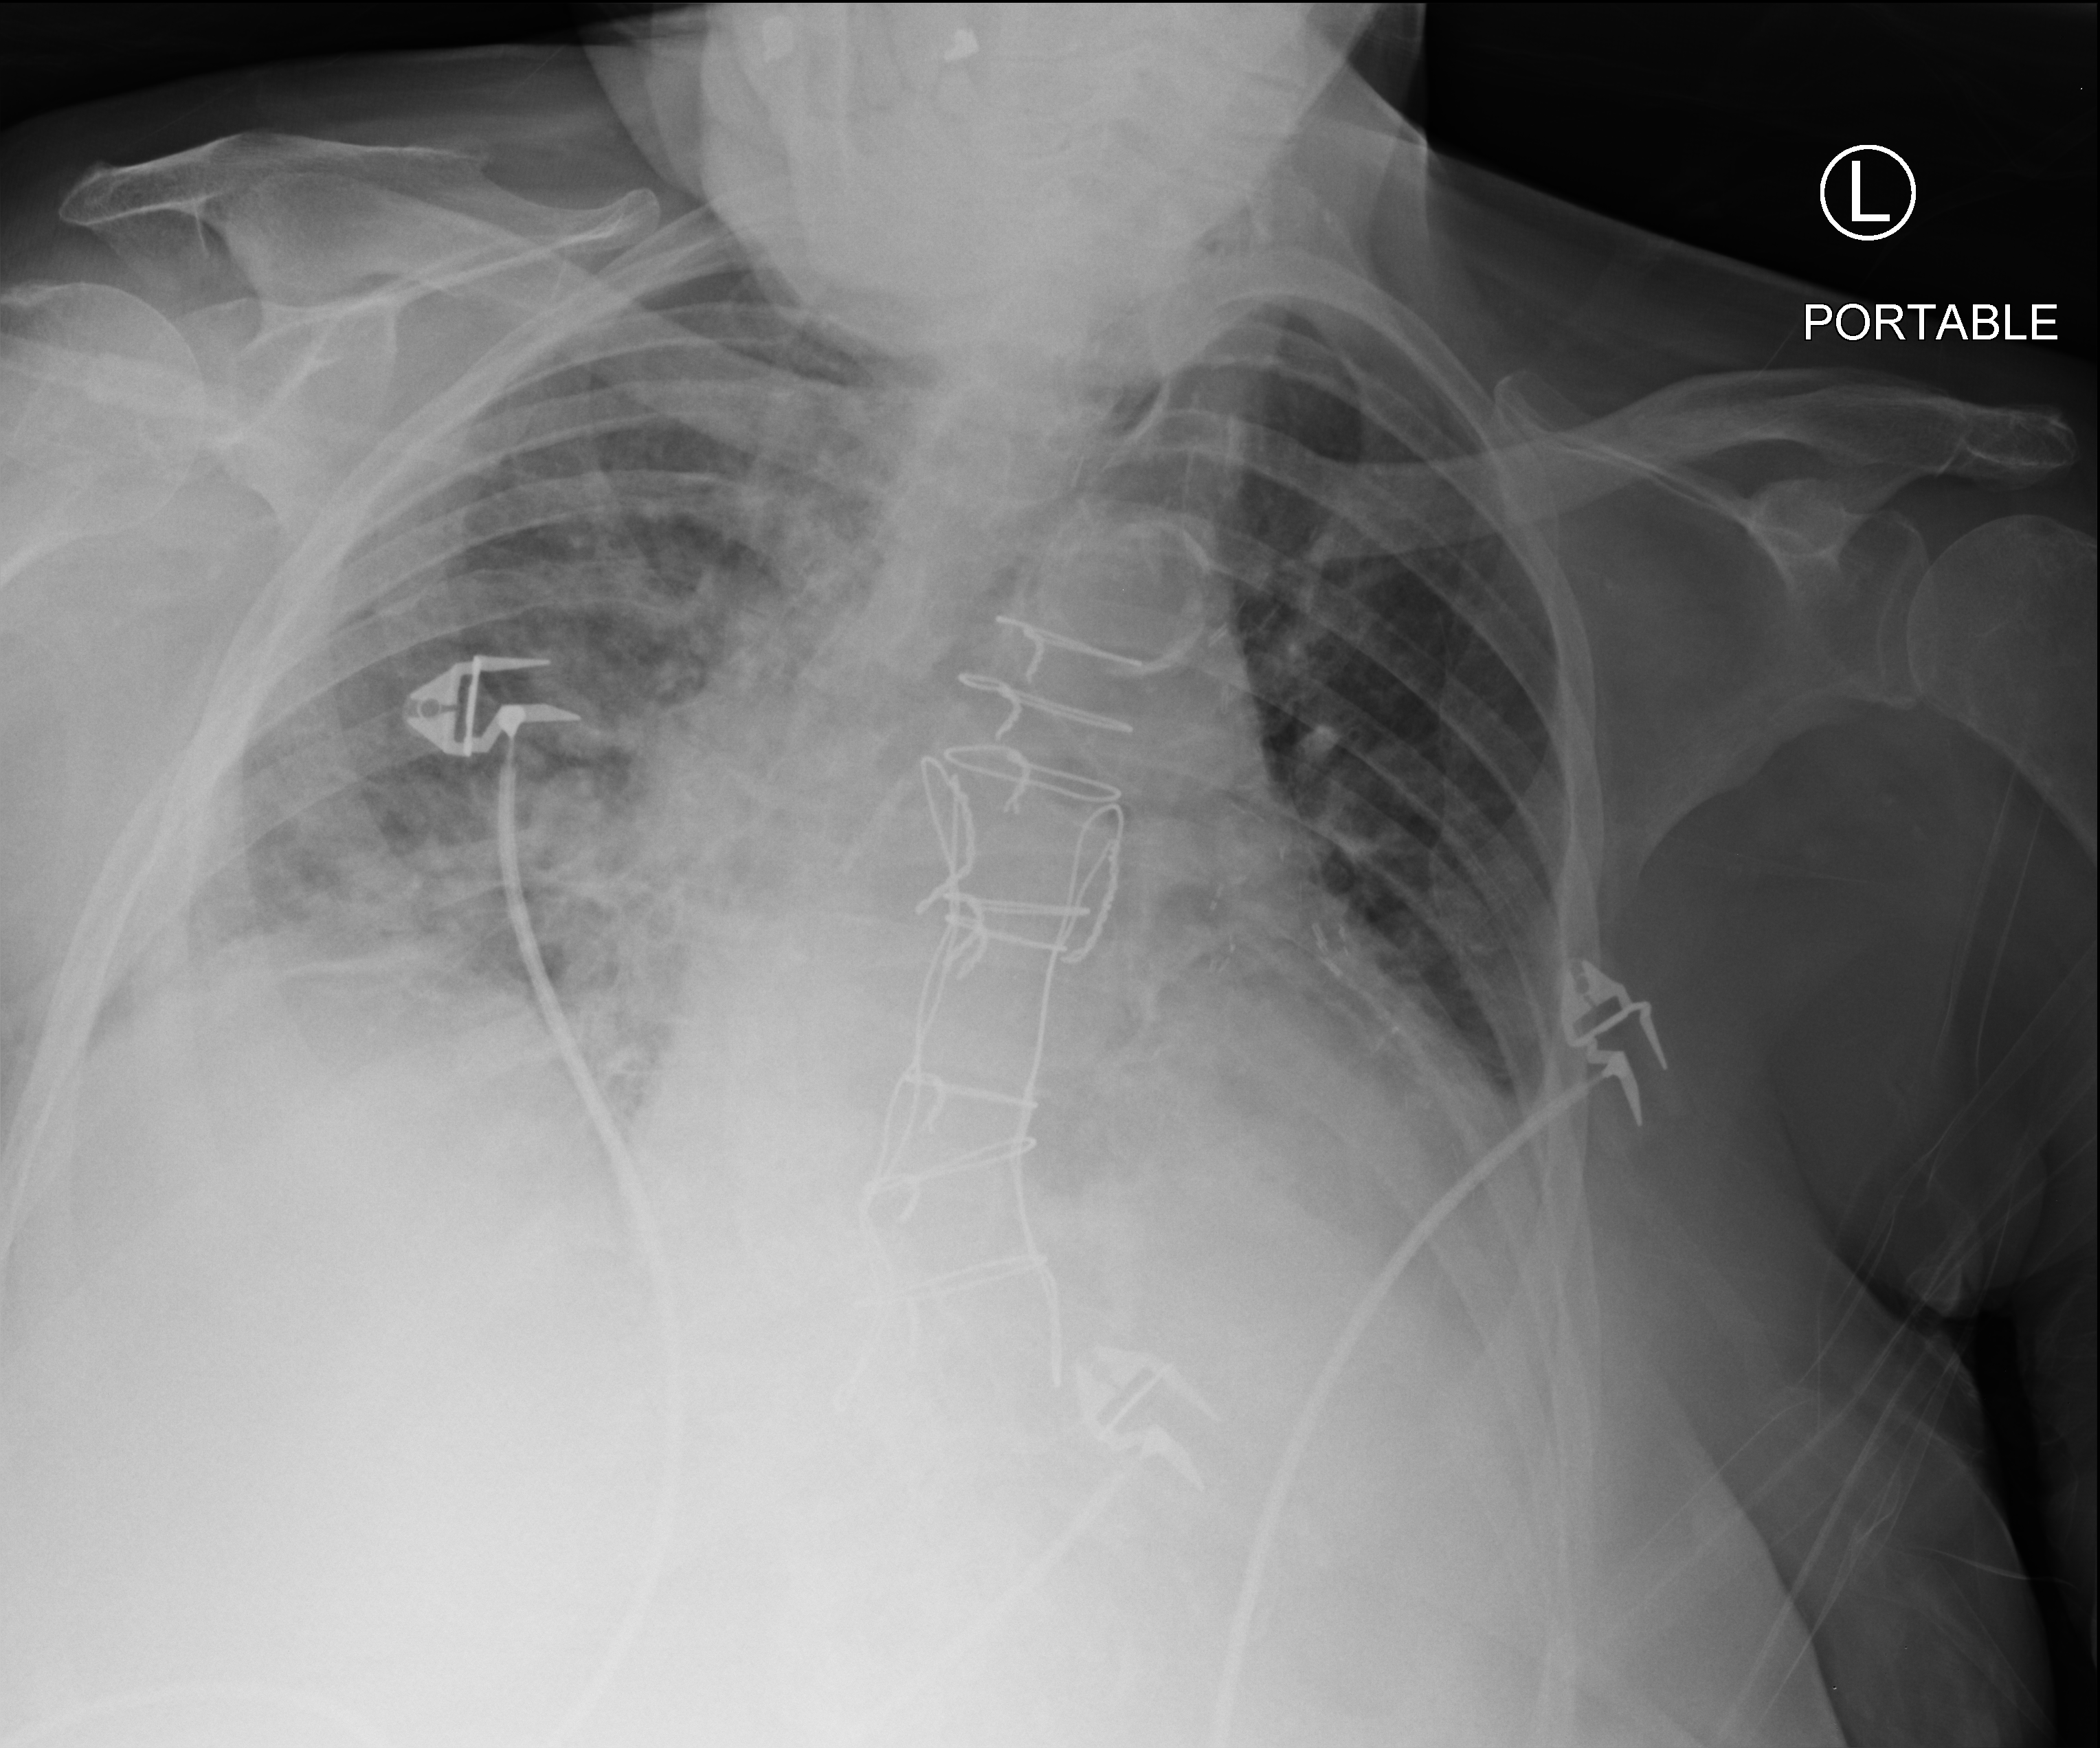
Chest X-ray (portable); anteroposterior (AP) projection. Patient hospitalised with COVID-19; female, aged 75–90 years.
Admission-level facts for this patient (not findings on this image; timing relative to this image not recorded):
- mechanically ventilated during this hospital stay: no
- length of hospital stay: 10 days